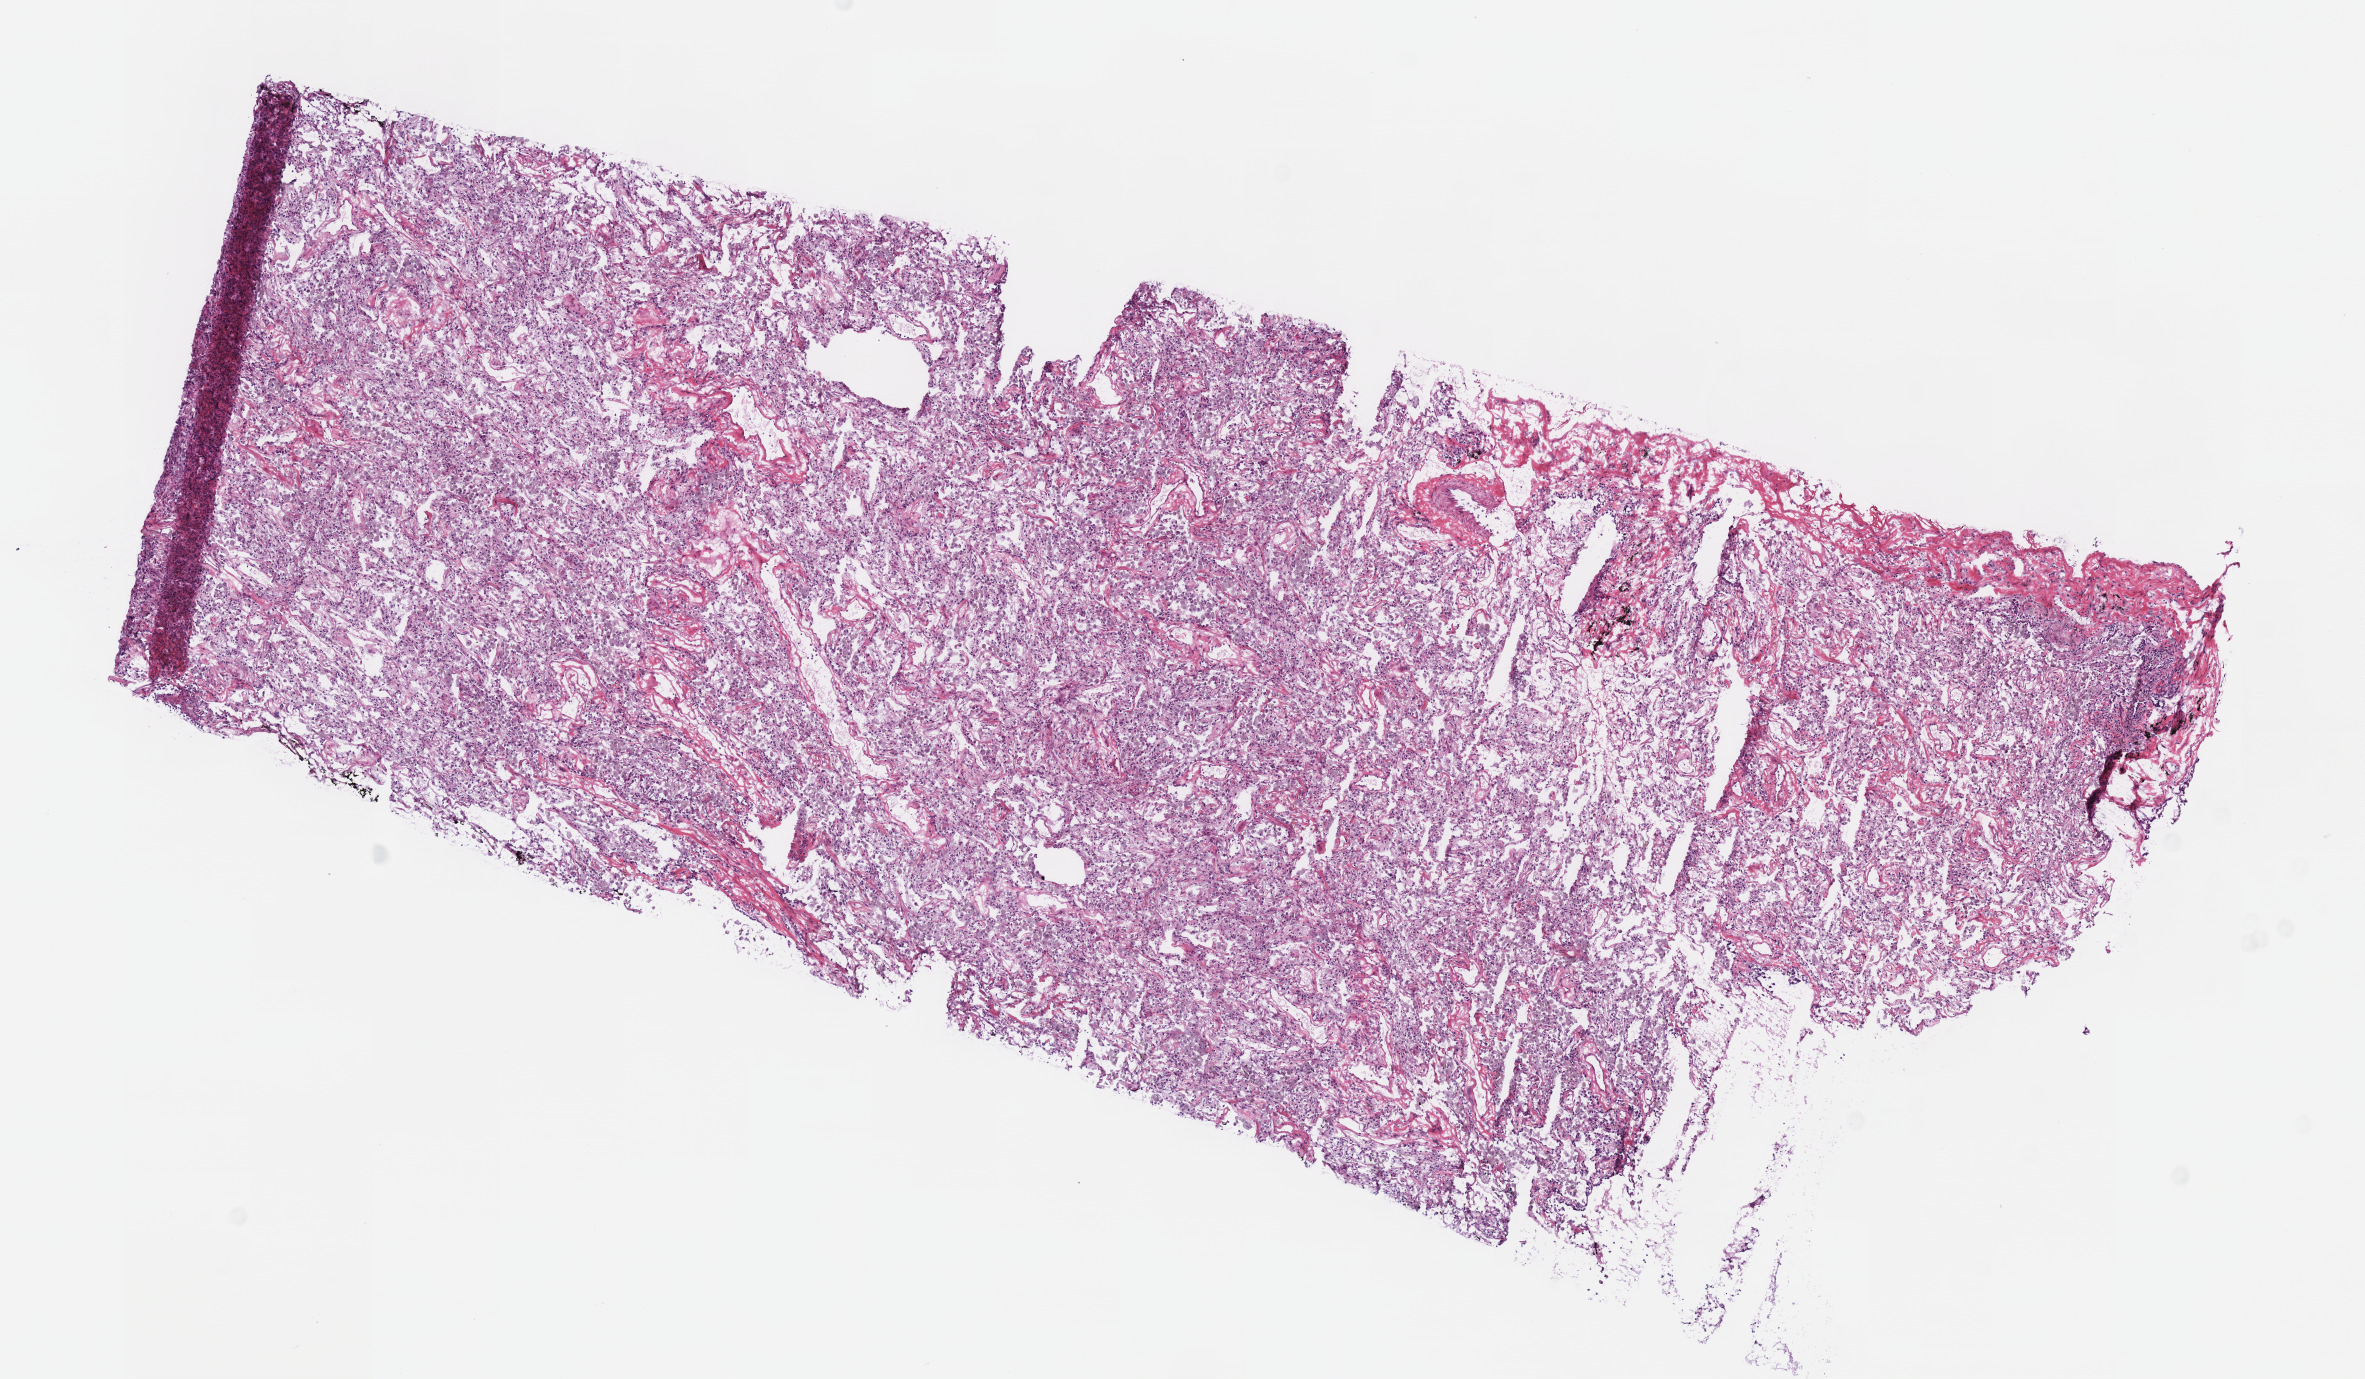
Digitized Hematoxylin and eosin (H&E) stained tissue section (whole slide), shown as a low-resolution overview of the whole scanned area (about 9.3 x 5.4 mm, from a 40x scan). Frozen section from the top of the tissue portion. Solid tissue normal (non-tumour tissue) sample from the lung. Male, age 67 years at initial diagnosis.
This section: solid tissue normal (non-tumour) sample from the same patient. Patient diagnosis: Adenocarcinoma, NOS (middle lobe, lung).